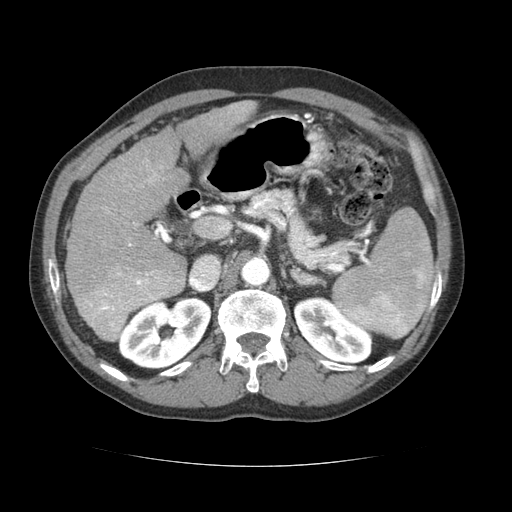
Contrast-enhanced abdominal CT (liver protocol), one axial slice; position 40 of 69 along the scan axis; 120 kVp; soft-tissue window (W 400 / L 40 HU); 2.5 mm slice thickness; 512 × 512 image matrix, field of view 360 × 360 mm. Case-level facts recorded for this patient, not image findings: diagnosis: hepatocellular carcinoma (patient treated with transarterial chemoembolisation; whether this scan precedes or follows treatment is not stated here); TNM stage (as recorded): Stage-II.
Outlined on this slice (semi-automatically segmented with operator editing):
- liver parenchyma outside the tumour (the mass and vessels are separate outlines, so this box may not span the whole liver): bounding box [x1, y1, x2, y2] px = [66, 100, 256, 340]
- mass: [76, 267, 183, 340]
- liver vessels: [107, 108, 244, 276]